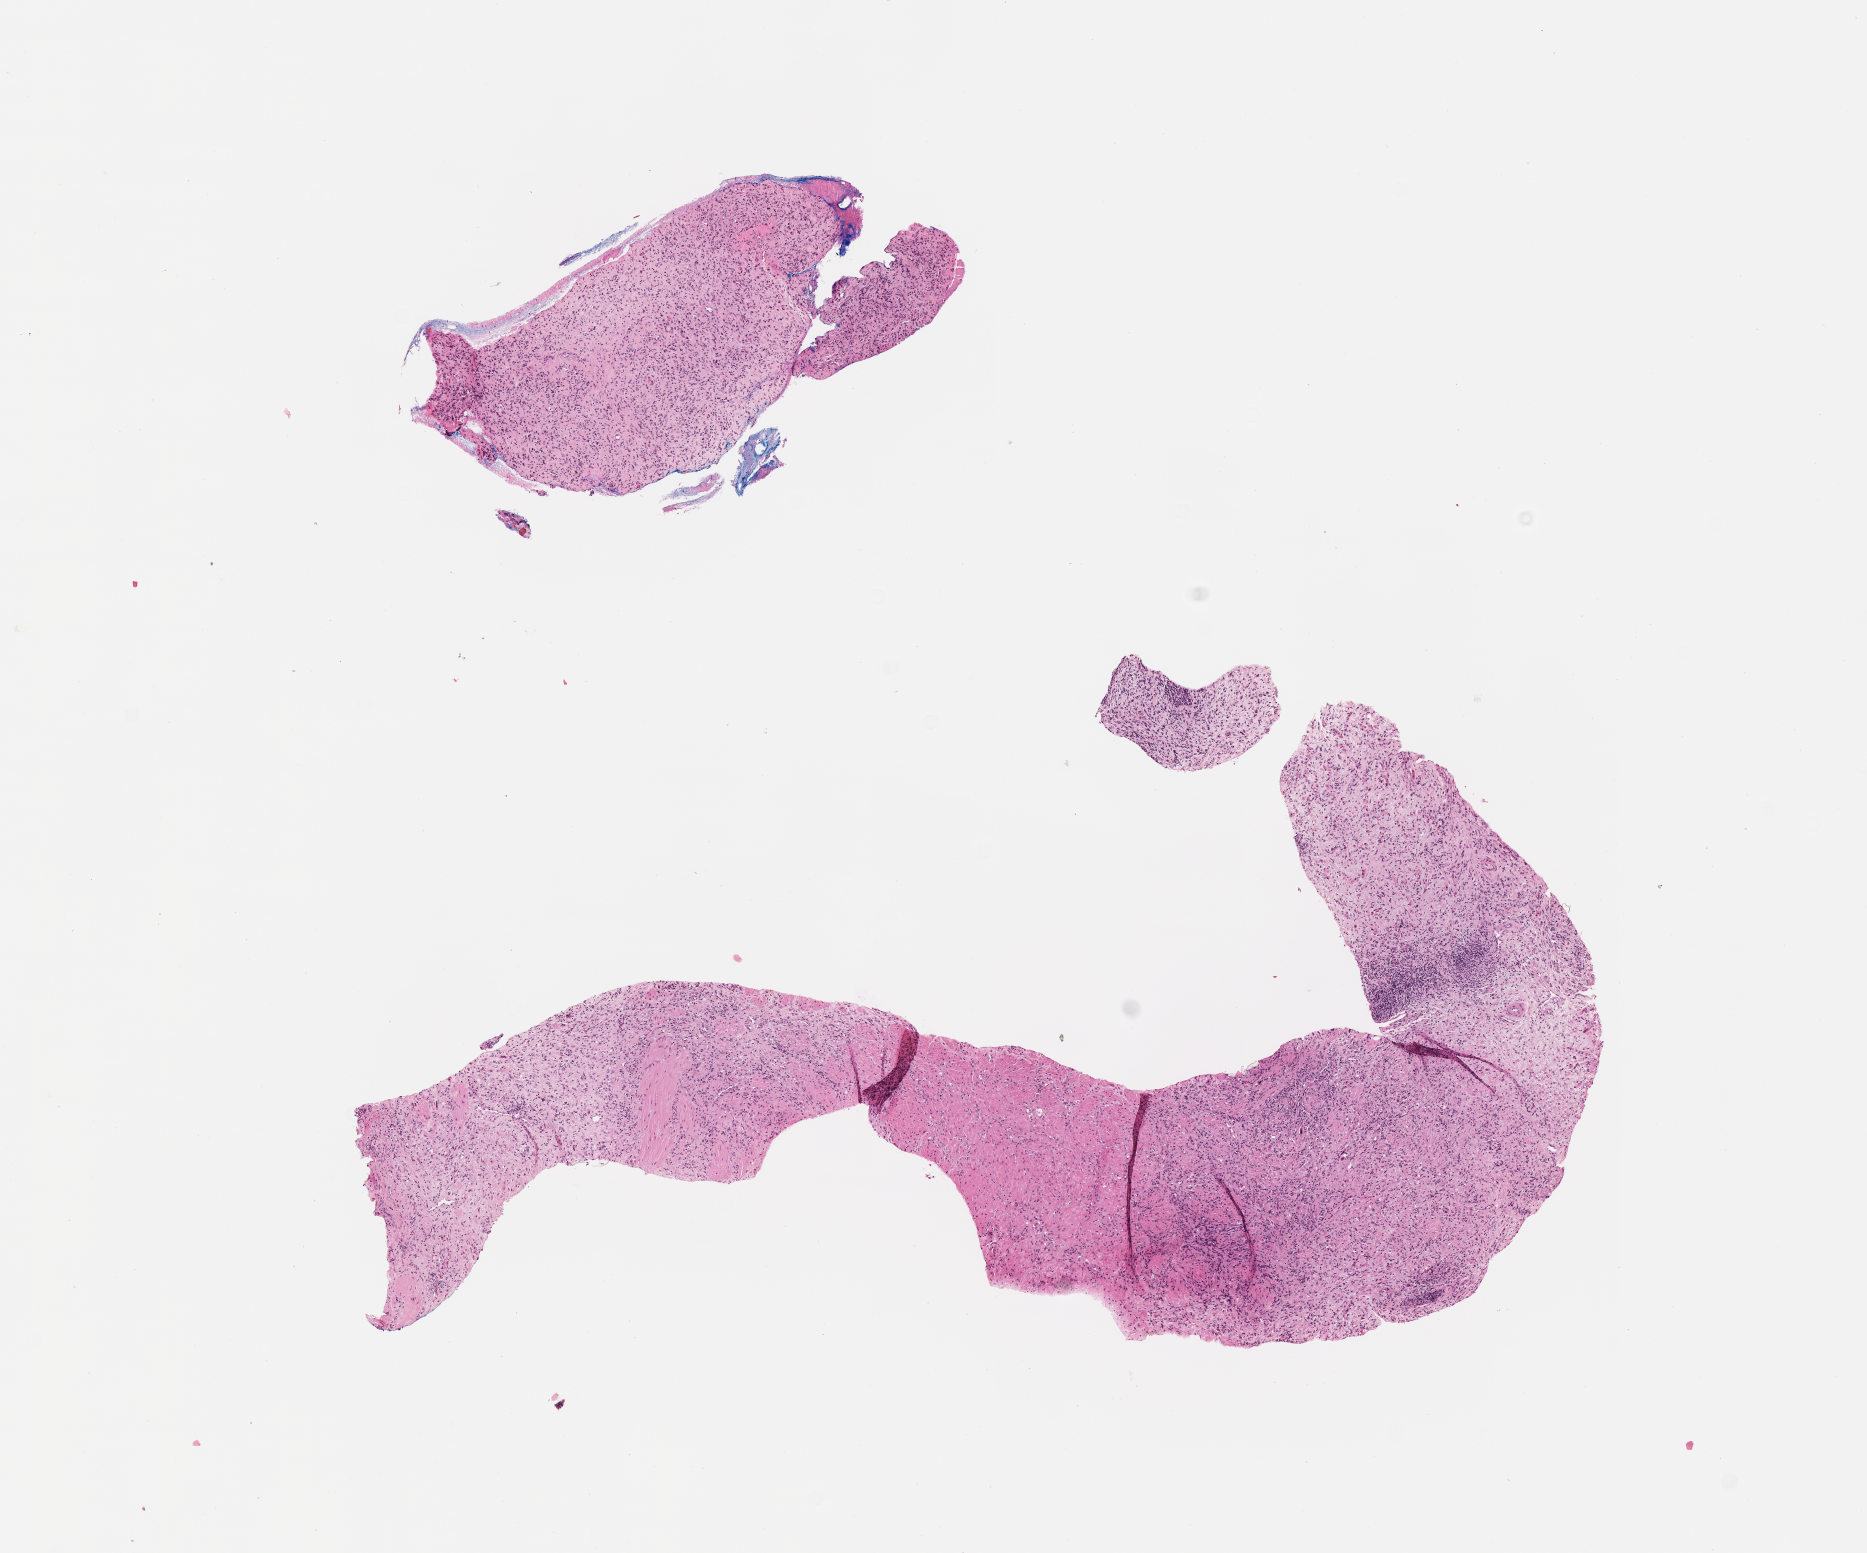
H&E whole-slide image of tumor tissue — a low-resolution overview of the entire scanned area, about 7.5 x 6.3 mm, formalin-fixed paraffin-embedded section, sample anatomic site: prostate. Male patient, age at diagnosis 15.7 years.
Stage (as recorded): 3. Diagnosis: rhabdomyosarcoma; histological classification: embryonal rhabdomyosarcoma.